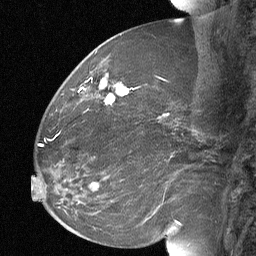
Breast MRI (dynamic contrast-enhanced), one sagittal slice. Position 28 of 64 along the scan axis. Dynamic contrast-enhanced study with each time point stored as its own series, time point 2 of 3 at this slice position (early post-contrast, ordered by acquisition time). 1.5 T. TE 4.8 ms, TR 27 ms. 2 mm slice thickness. 256 × 256 image matrix, field of view 200 × 200 mm. Patient: female, 60 years. From the clinical record (not read from this slice): setting: breast cancer imaged before/during neoadjuvant chemotherapy; receptor status: HR-positive, HER2-negative.
Structures marked on this image (semi-automatically segmented with operator editing):
- analysis volume of interest (the breast-tissue region the enhancement analysis was run in; not a lesion): bounding box [x1, y1, x2, y2] px = [92, 70, 129, 106]
- tumour enhancement mask (voxels above the 90 % enhancement threshold inside the analysis volume of interest): [101, 80, 129, 104]